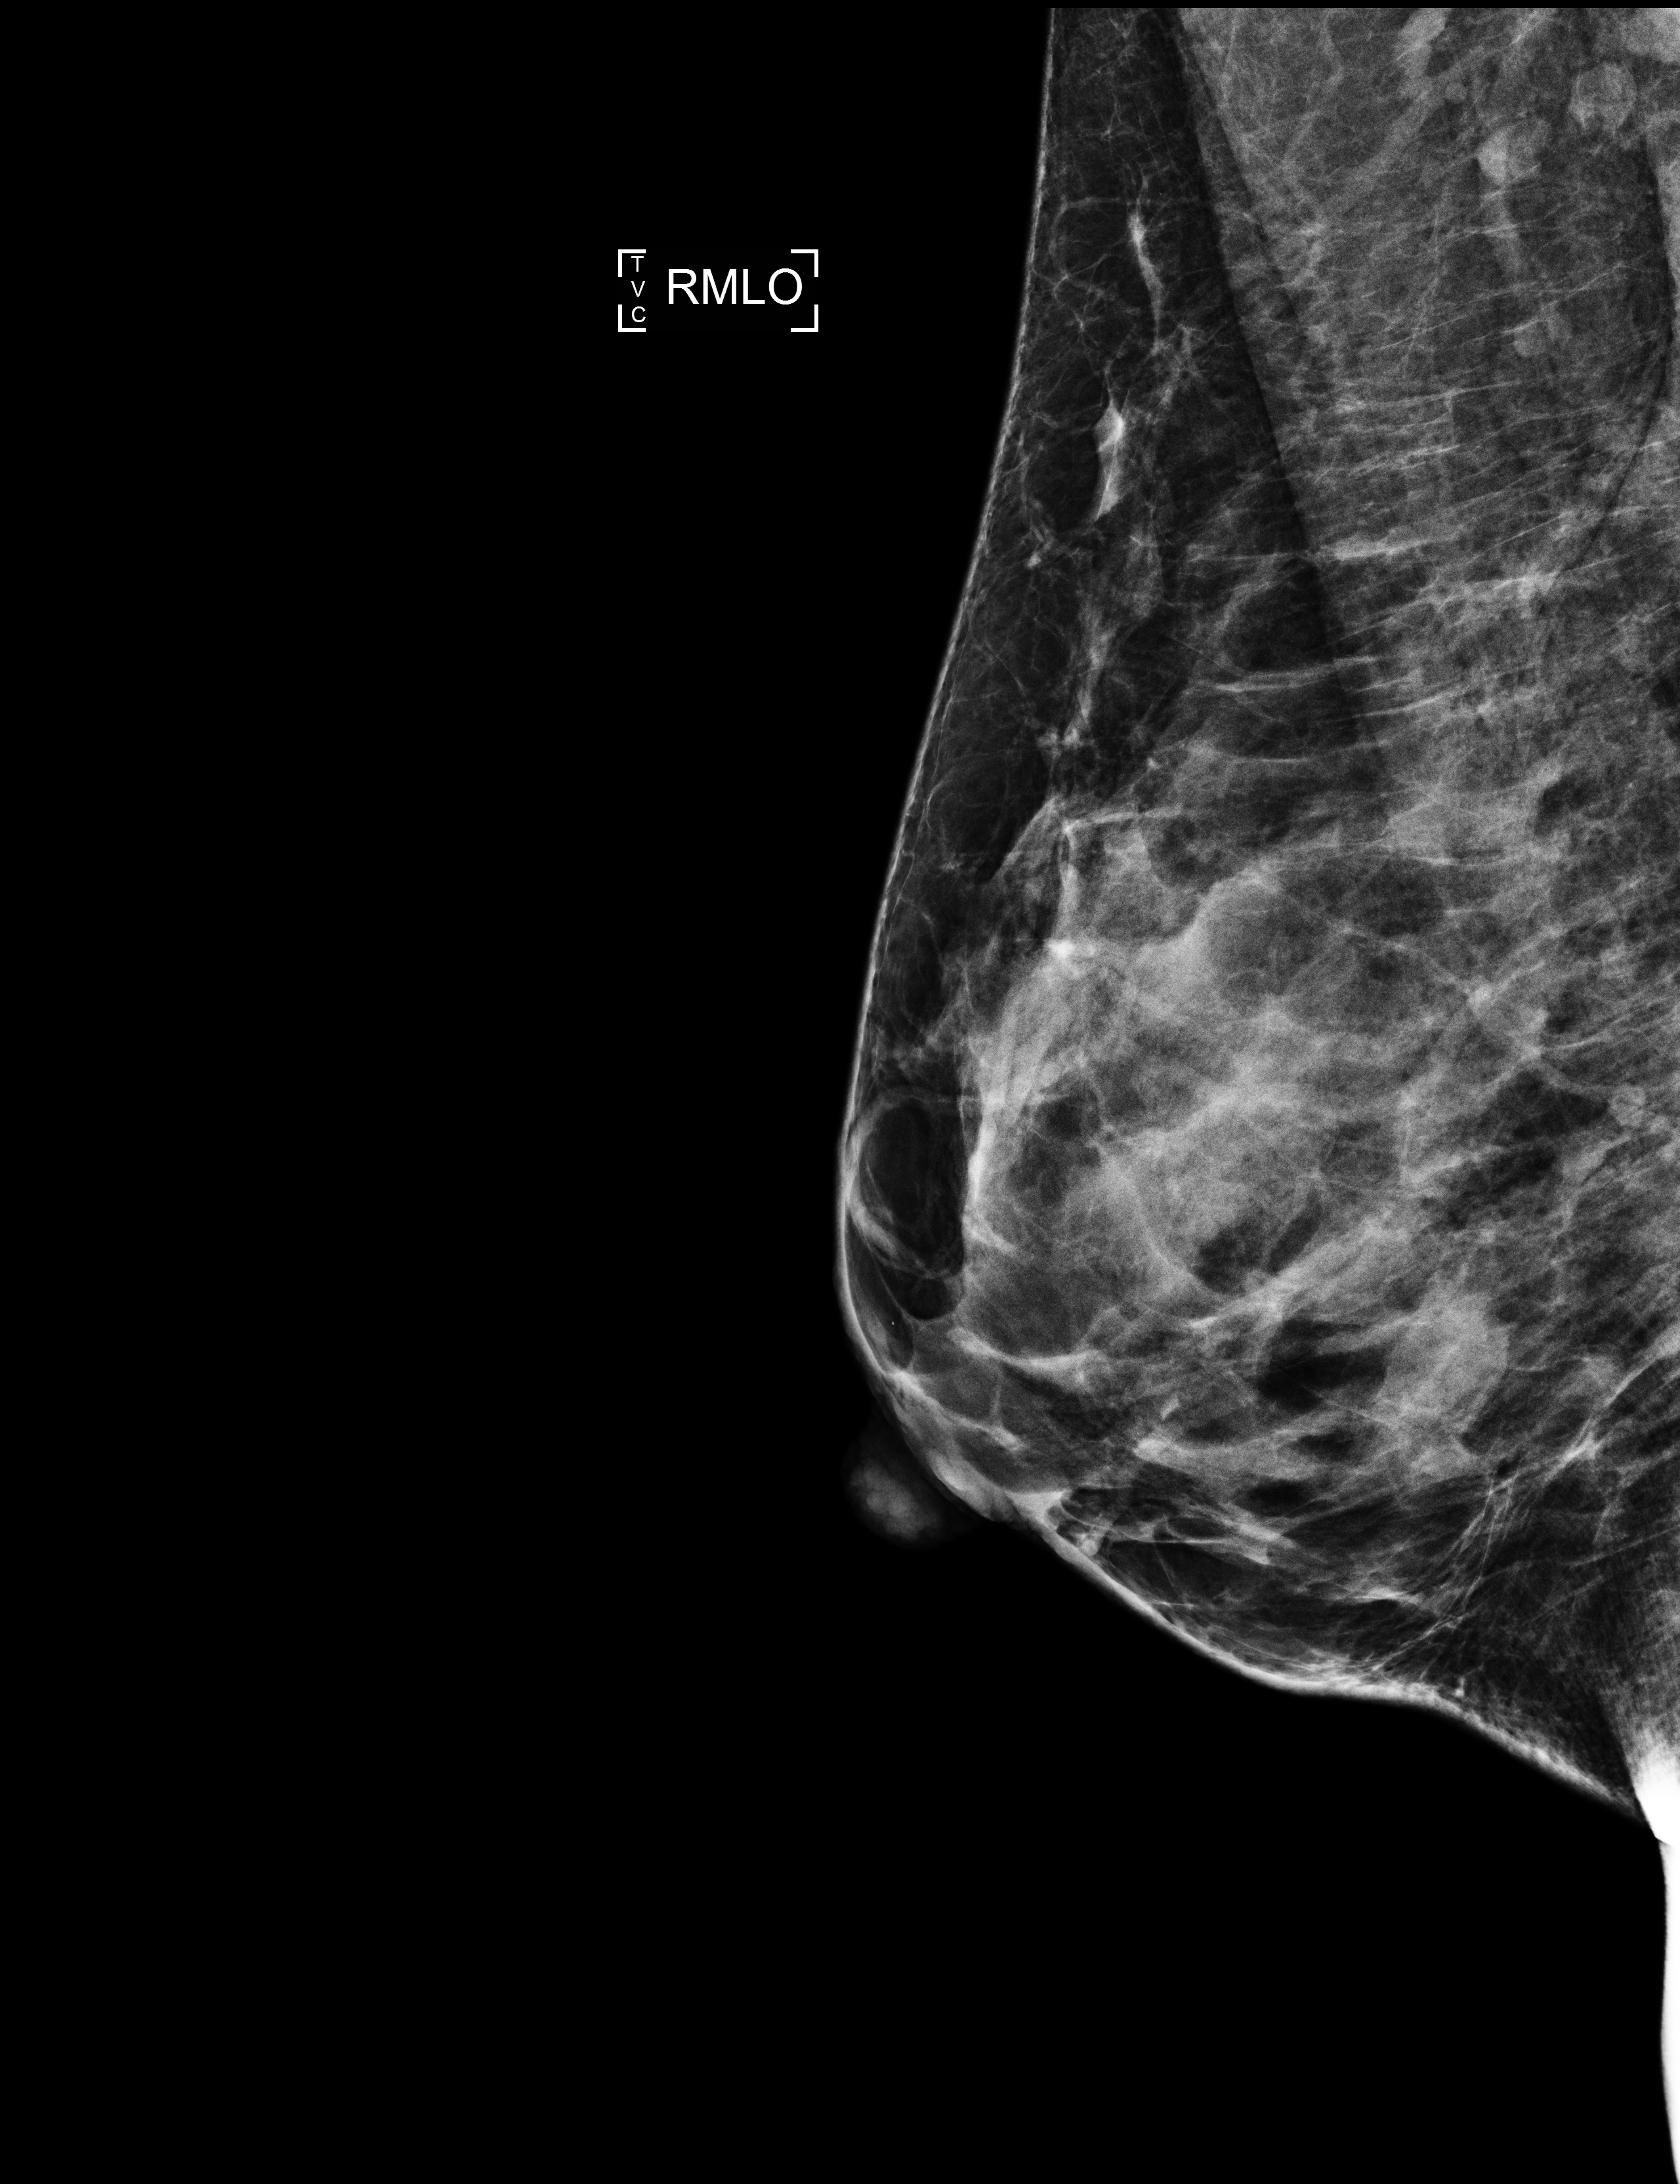
Screening examination. Patient aged 50 years (female).
Image type: full-field digital mammogram. Breast: right. Projection: mediolateral oblique (MLO) view.